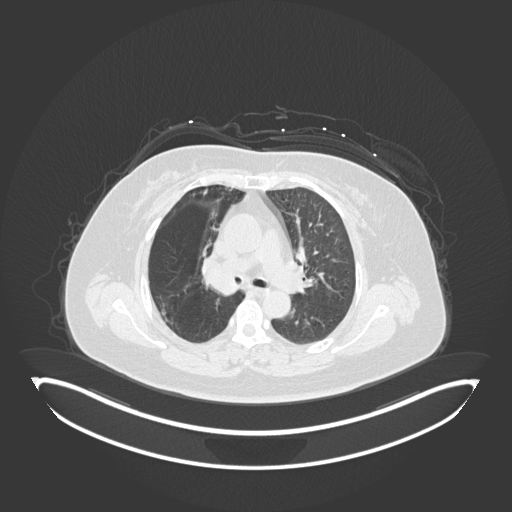
Chest CT, one axial slice; slice 108 of 245 in the series (ordered by position); 120 kVp; lung window (W 1500 / L -600 HU); 1 mm slice thickness; 512 × 512 image matrix. Patient: female, 60 years. From the clinical record (not read from this slice): clinical TNM (as recorded): T1c N0 M0.
Annotated regions visible in this slice (rectangle marked by the reading radiologist):
- lung tumour (recorded histology: squamous cell carcinoma): box from (x=198, y=253) to (x=240, y=298) px